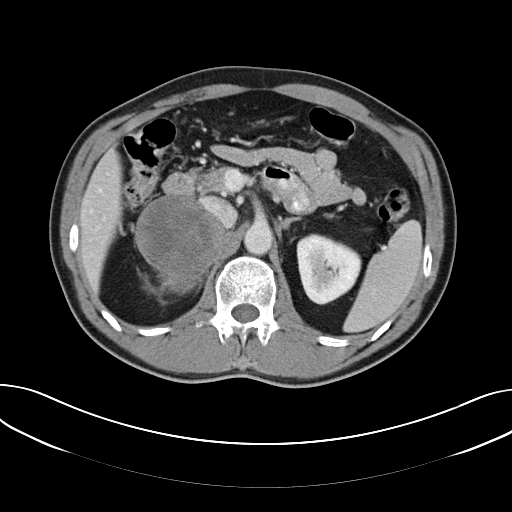
Contrast-enhanced abdominal CT, one axial slice. Position 33 of 61 along the scan axis. Reconstruction kernel B40f. 120 kVp. Intravenous contrast given. Soft-tissue window (W 400 / L 40 HU). 5 mm slice thickness. 512 × 512 image matrix, field of view 372 × 372 mm. Patient: male, 57 years. Case-level facts recorded for this patient, not image findings: diagnosis: adrenocortical carcinoma; tumour side: right adrenal; tumour size at pathology: 11.2 cm.
Annotated regions visible in this slice (semi-automatic segmentation, software-assisted and operator-edited):
- mass: bounding box <137,196,225,291> (left, top, right, bottom; pixels)